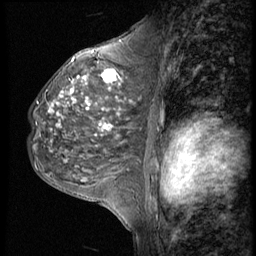
Breast MRI (dynamic contrast-enhanced), one sagittal slice; slice 30 of 56 in the series (ordered by position); 4 images stored at this slice position (order not interpretable as contrast timing); 1.5 T; TE 4.2 ms, TR 9 ms; 2.5 mm slice thickness; 256 × 256 image matrix. Female patient, age 50 years. From the clinical record (not read from this slice): setting: breast cancer imaged before/during neoadjuvant chemotherapy; receptor status: triple-negative.
Structures marked on this image (semi-automatically segmented with operator editing):
- analysis volume of interest (the breast-tissue region the enhancement analysis was run in; not a lesion): box from (x=27, y=46) to (x=148, y=188) px
- tumour enhancement mask (voxels above the 140 % enhancement threshold inside the analysis volume of interest): (x=49, y=70)–(x=124, y=131)